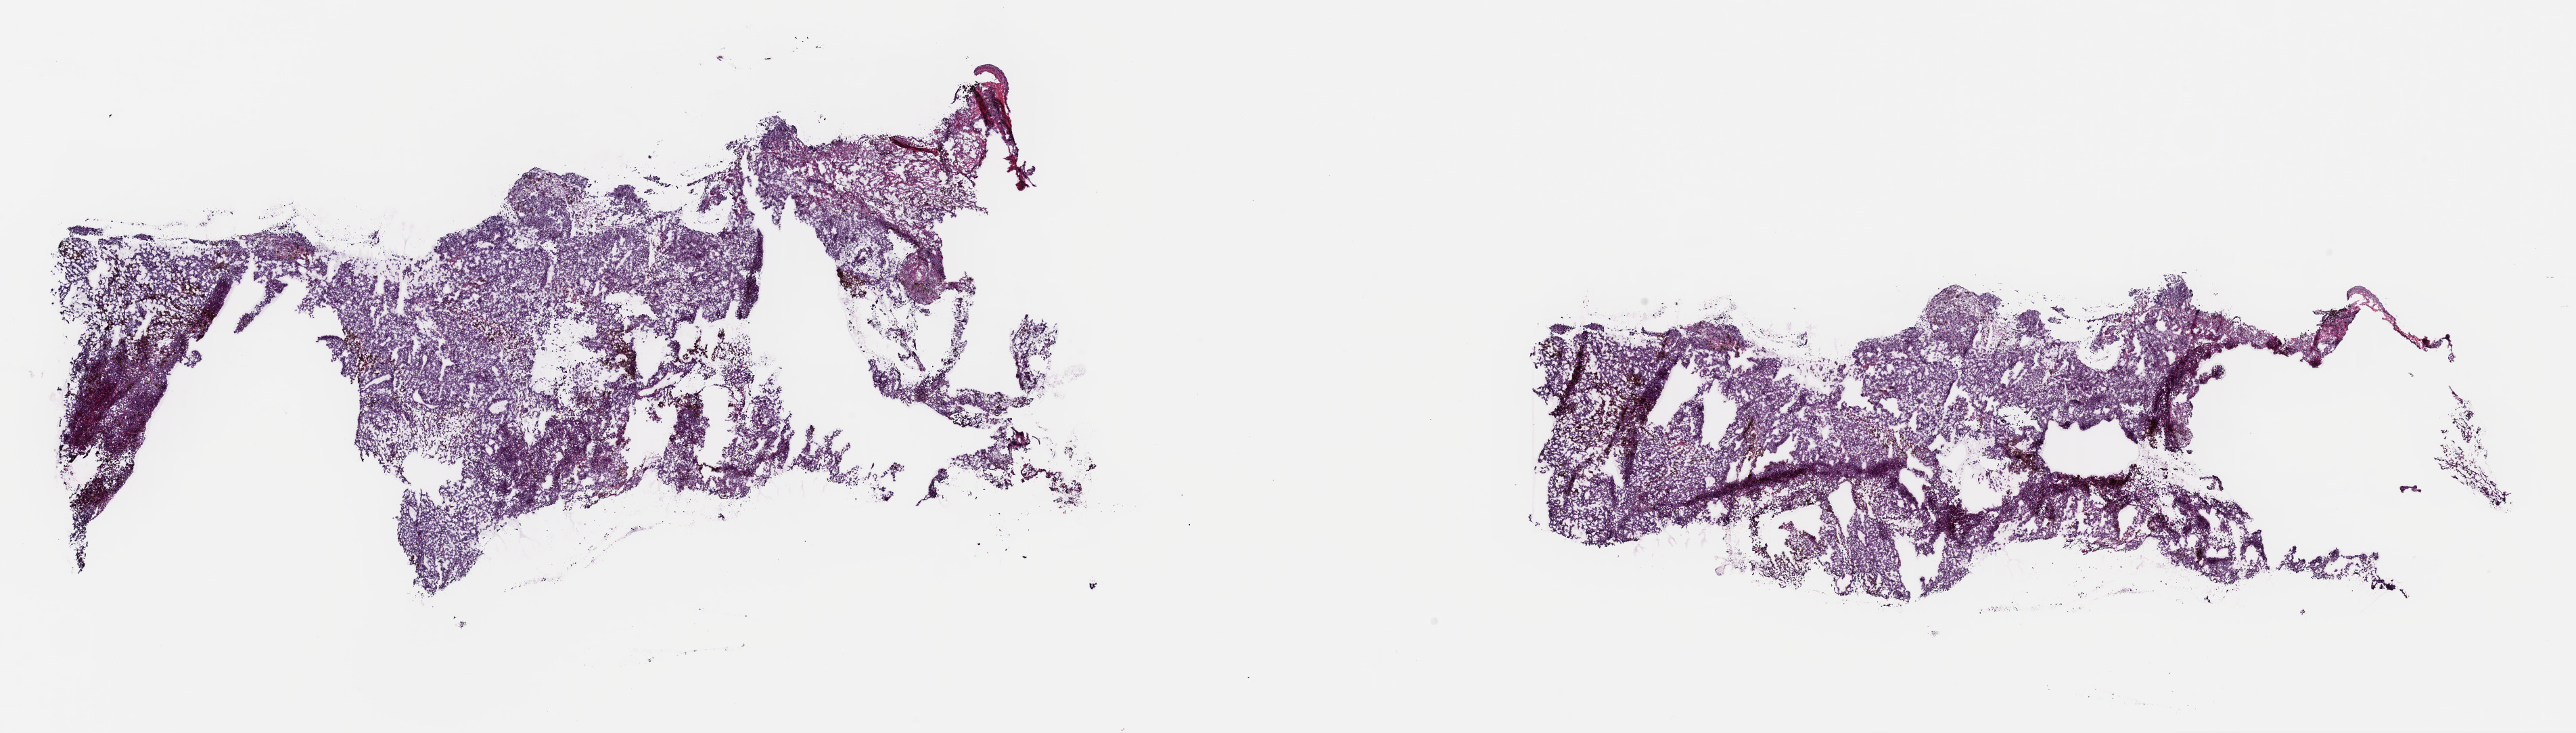
Digitized H&E-stained tissue section (whole slide) — low-resolution overview of the scanned area, about 30.1 x 8.6 mm (from a 40x scan), frozen section, metastatic tumour sample, sampled site not recorded. Male patient; age at initial diagnosis 55 years. Slide review estimates, as recorded: tumour cells 100%, tumour nuclei 92%, normal cells 0%, stromal cells 0%, necrosis 0%. Infiltration values recorded for this section: lymphocyte infiltration 0%, monocyte infiltration 0%, neutrophil infiltration 0%.
This section: metastatic tumour tissue. Patient diagnosis: Malignant melanoma, NOS.